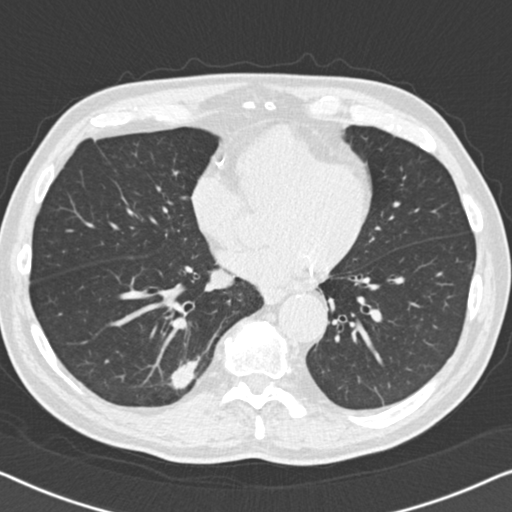
Low-dose screening chest CT, axial slice, second screening round (one year after baseline), lung window (W 1500 / L -600 HU), 2 mm slice thickness, standard (soft-tissue) reconstruction kernel (B30f), 120 kVp. Male participant, aged 74 years at enrolment. Current smoker at enrolment.
- Expert reader's lesion annotation, bounding box <148,343,217,408> (left, top, right, bottom; pixels).
- The screening reader recorded 5 non-calcified nodules or masses ≥4 mm on this exam; which of them this box marks is not recorded.
- Participant outcome: lung cancer diagnosed 55 days after this screen — bronchiolo-alveolar adenocarcinoma, NOS, right lower lobe, moderately differentiated (G2), stage IA (AJCC 6th edition), 16 mm at pathology.